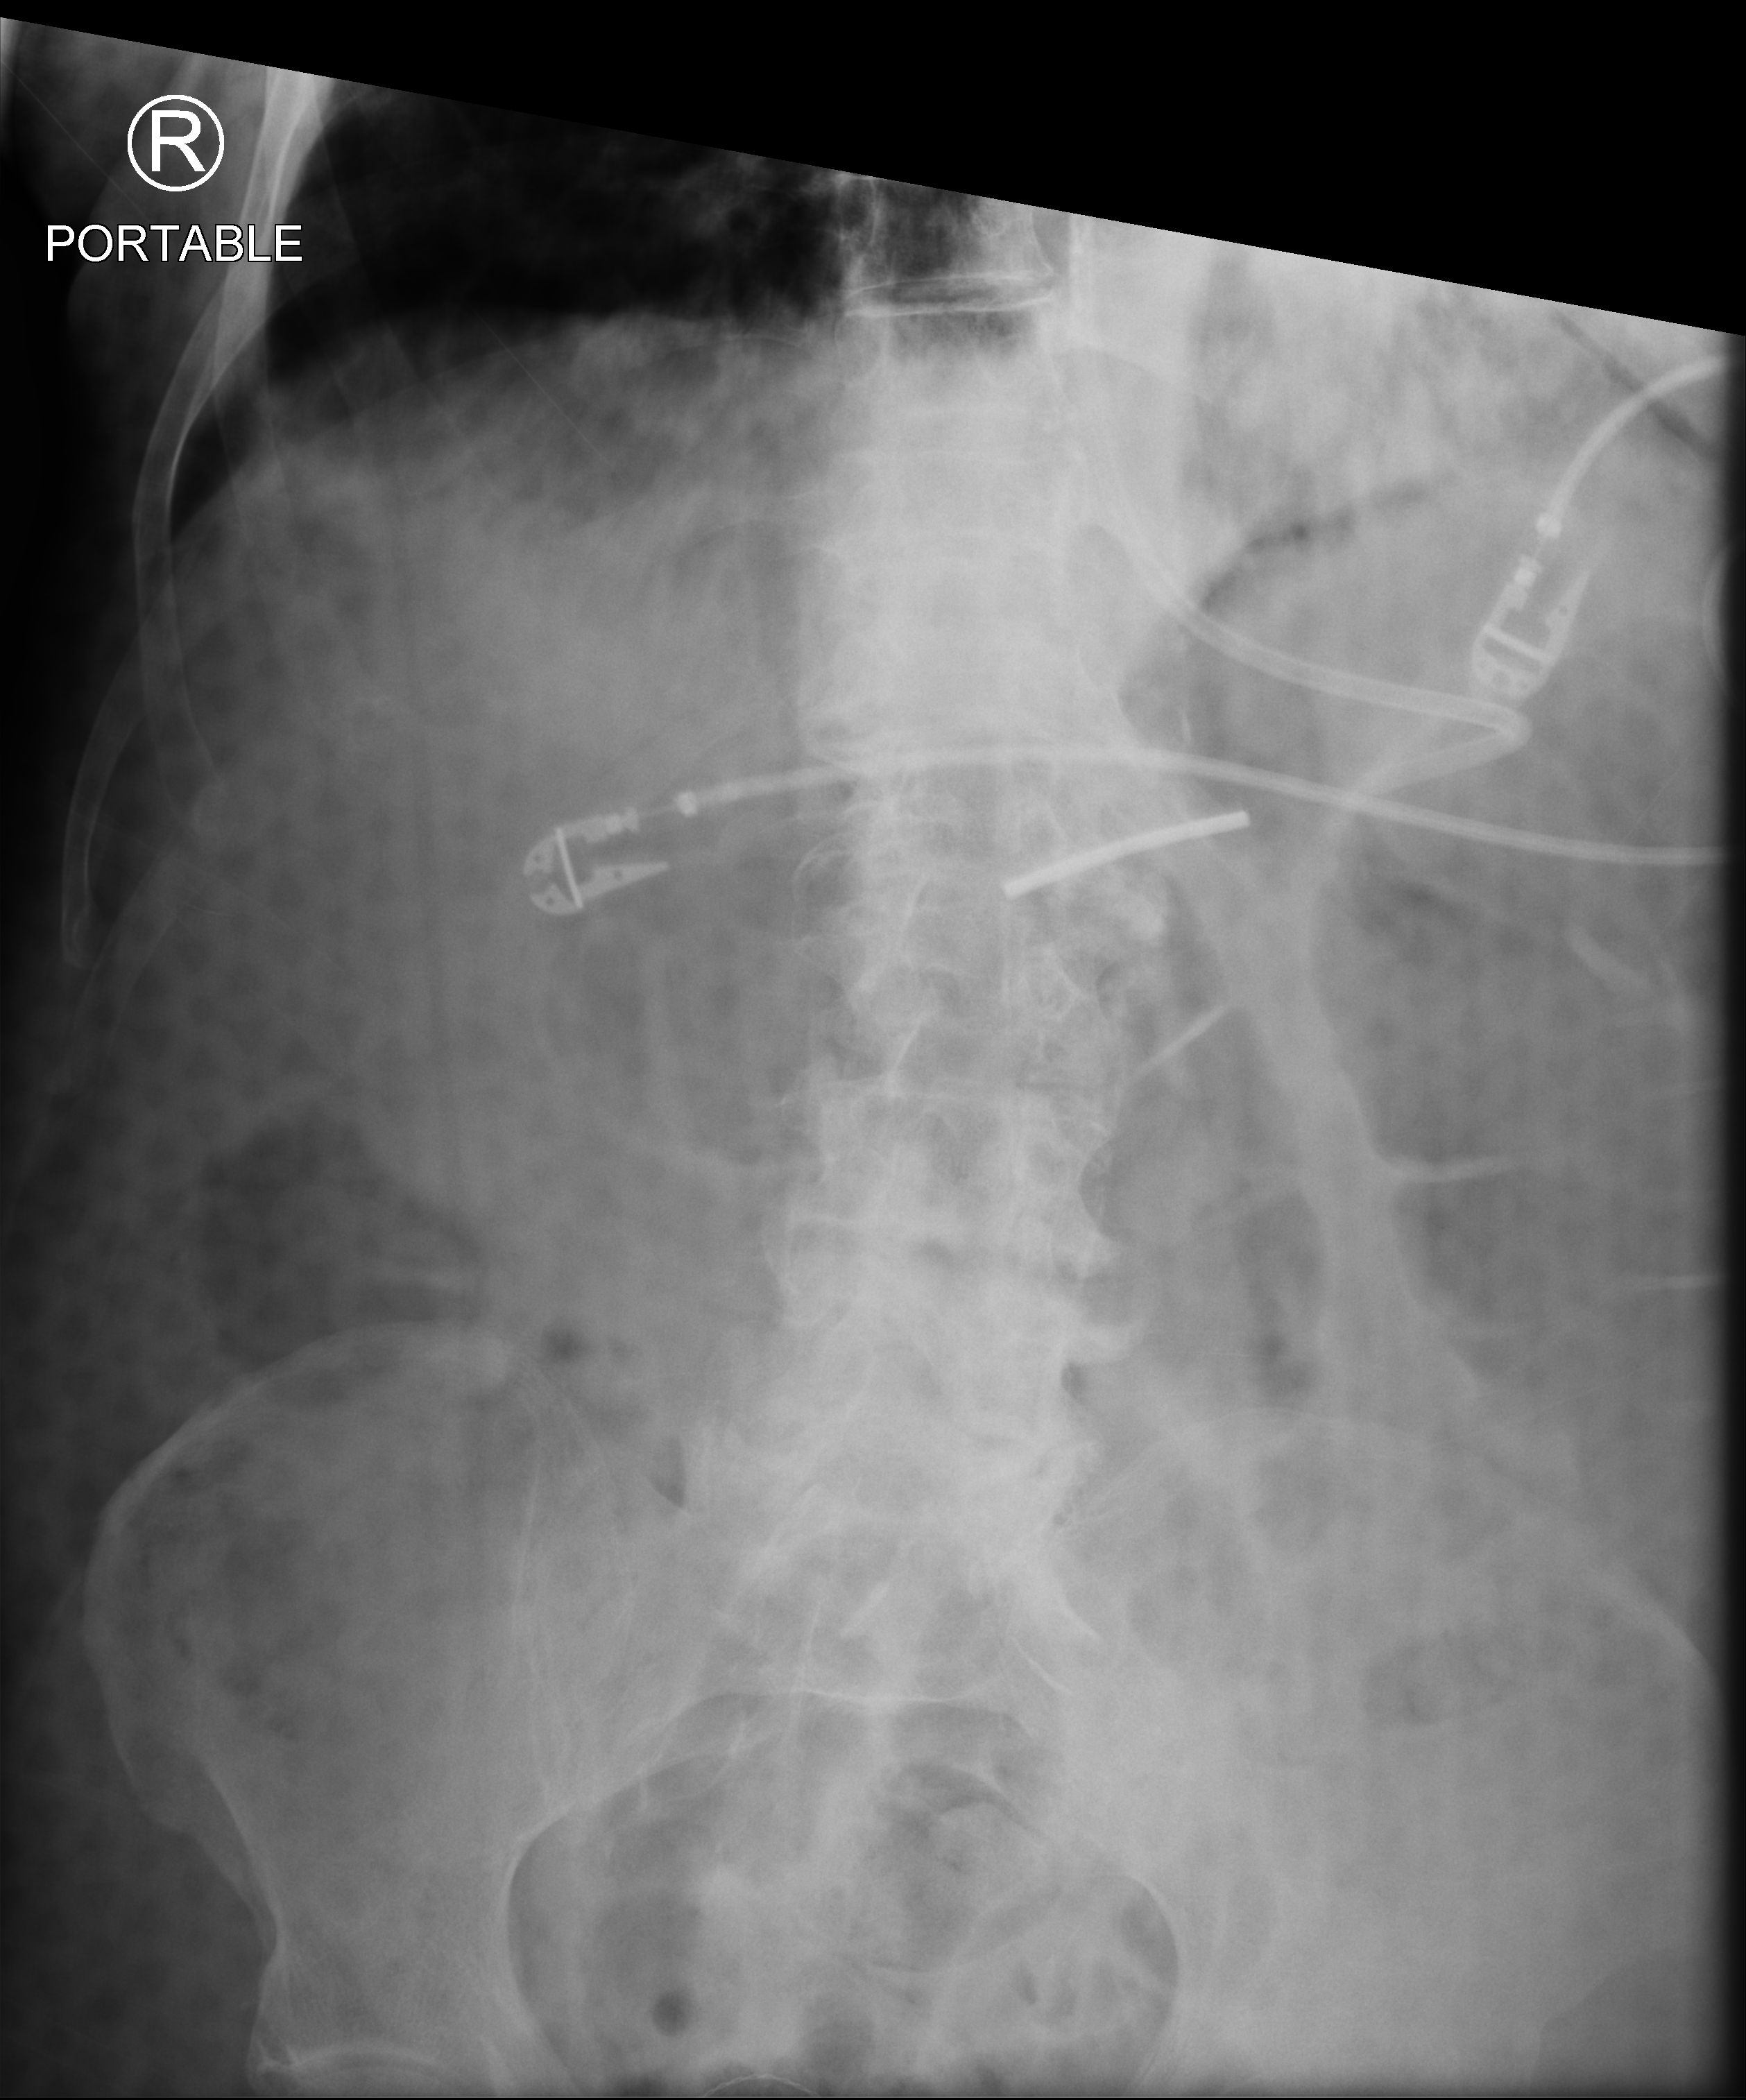
Portable abdomen radiograph, anteroposterior (AP) projection. Patient hospitalised with COVID-19; male, aged 75–90 years.
Hospital-stay facts (about this admission, not read from this image; timing relative to this image not recorded): length of hospital stay: 26 days.